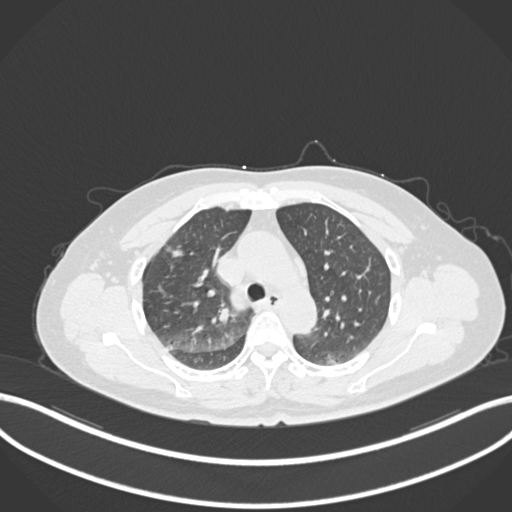
Chest CT, one axial slice; slice 163 of 223 in the series (ordered by position); reconstruction kernel B30f; 120 kVp; lung window (W 1500 / L -600 HU); 1 mm slice thickness; 512 × 512 image matrix, field of view 400 × 400 mm. Patient: female, 56 years. Case-level facts recorded for this patient, not image findings: clinical TNM (as recorded): T1c N0 M0.
Structures marked on this image (bounding box drawn by a radiologist):
- lung tumour (recorded histology: adenocarcinoma): box from (x=167, y=243) to (x=190, y=262) px